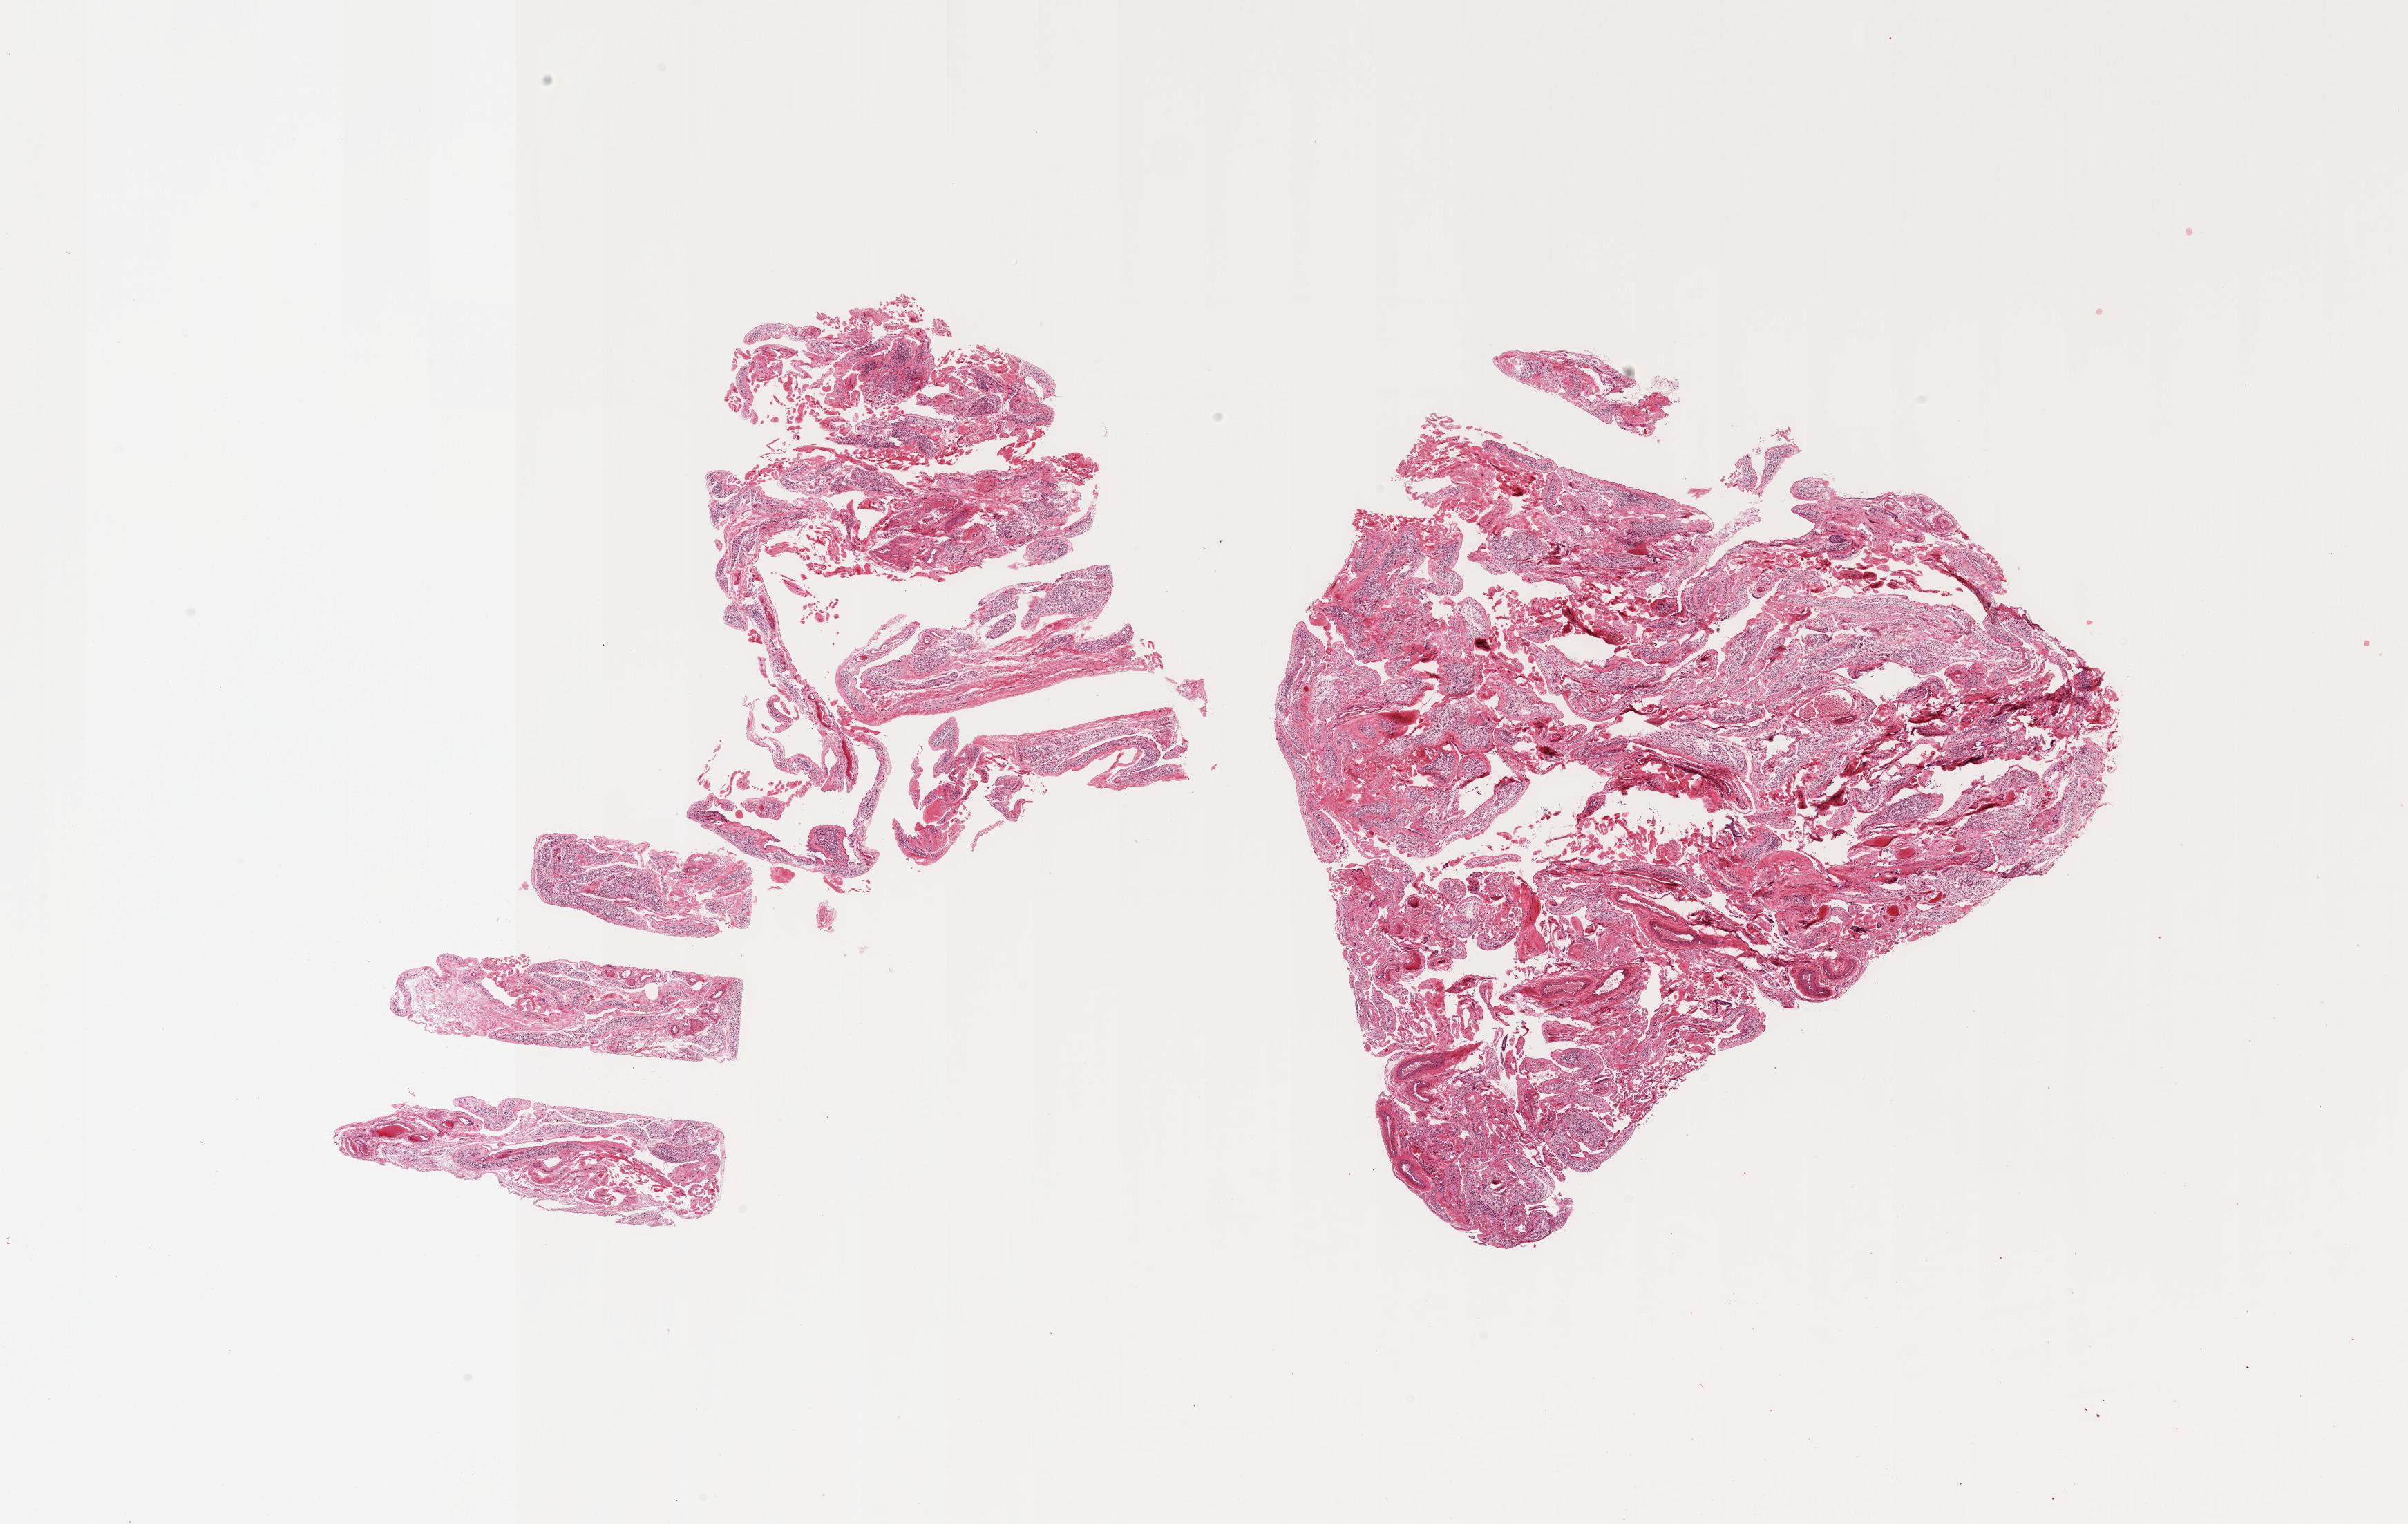
Digitized hematoxylin and eosin (H&E)-stained section — shown as a low-resolution overview of the whole scanned area (about 27.6 x 17.4 mm, acquisition: 20x scan); PAXgene-fixed, paraffin-embedded tissue; target tissue: omentum; donor tissue sample. Donor: male.
* reviewer comment on this tissue sample: 2 pieces; atrophy of fat